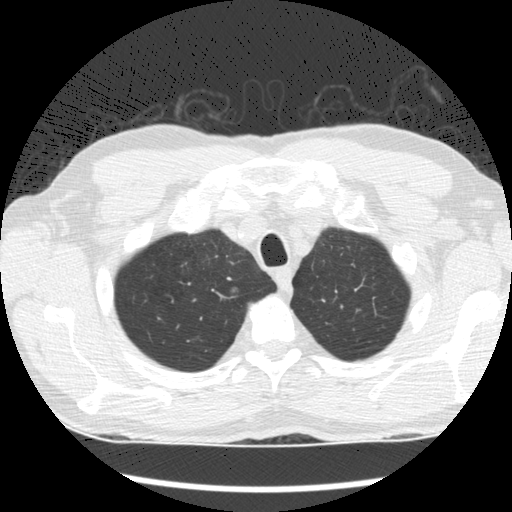
Low-dose screening chest CT, one axial slice. Position 138 of 164 along the scan axis. Reconstruction kernel STANDARD. 120 kVp. Lung window (W 1500 / L -600 HU). 512 × 512 image matrix, field of view 340 × 340 mm.
Structures marked on this image (manually delineated by an expert):
- lesion 1 (tumor, upper lobe of right lung): bounding box [x1, y1, x2, y2] px = [231, 286, 240, 294]